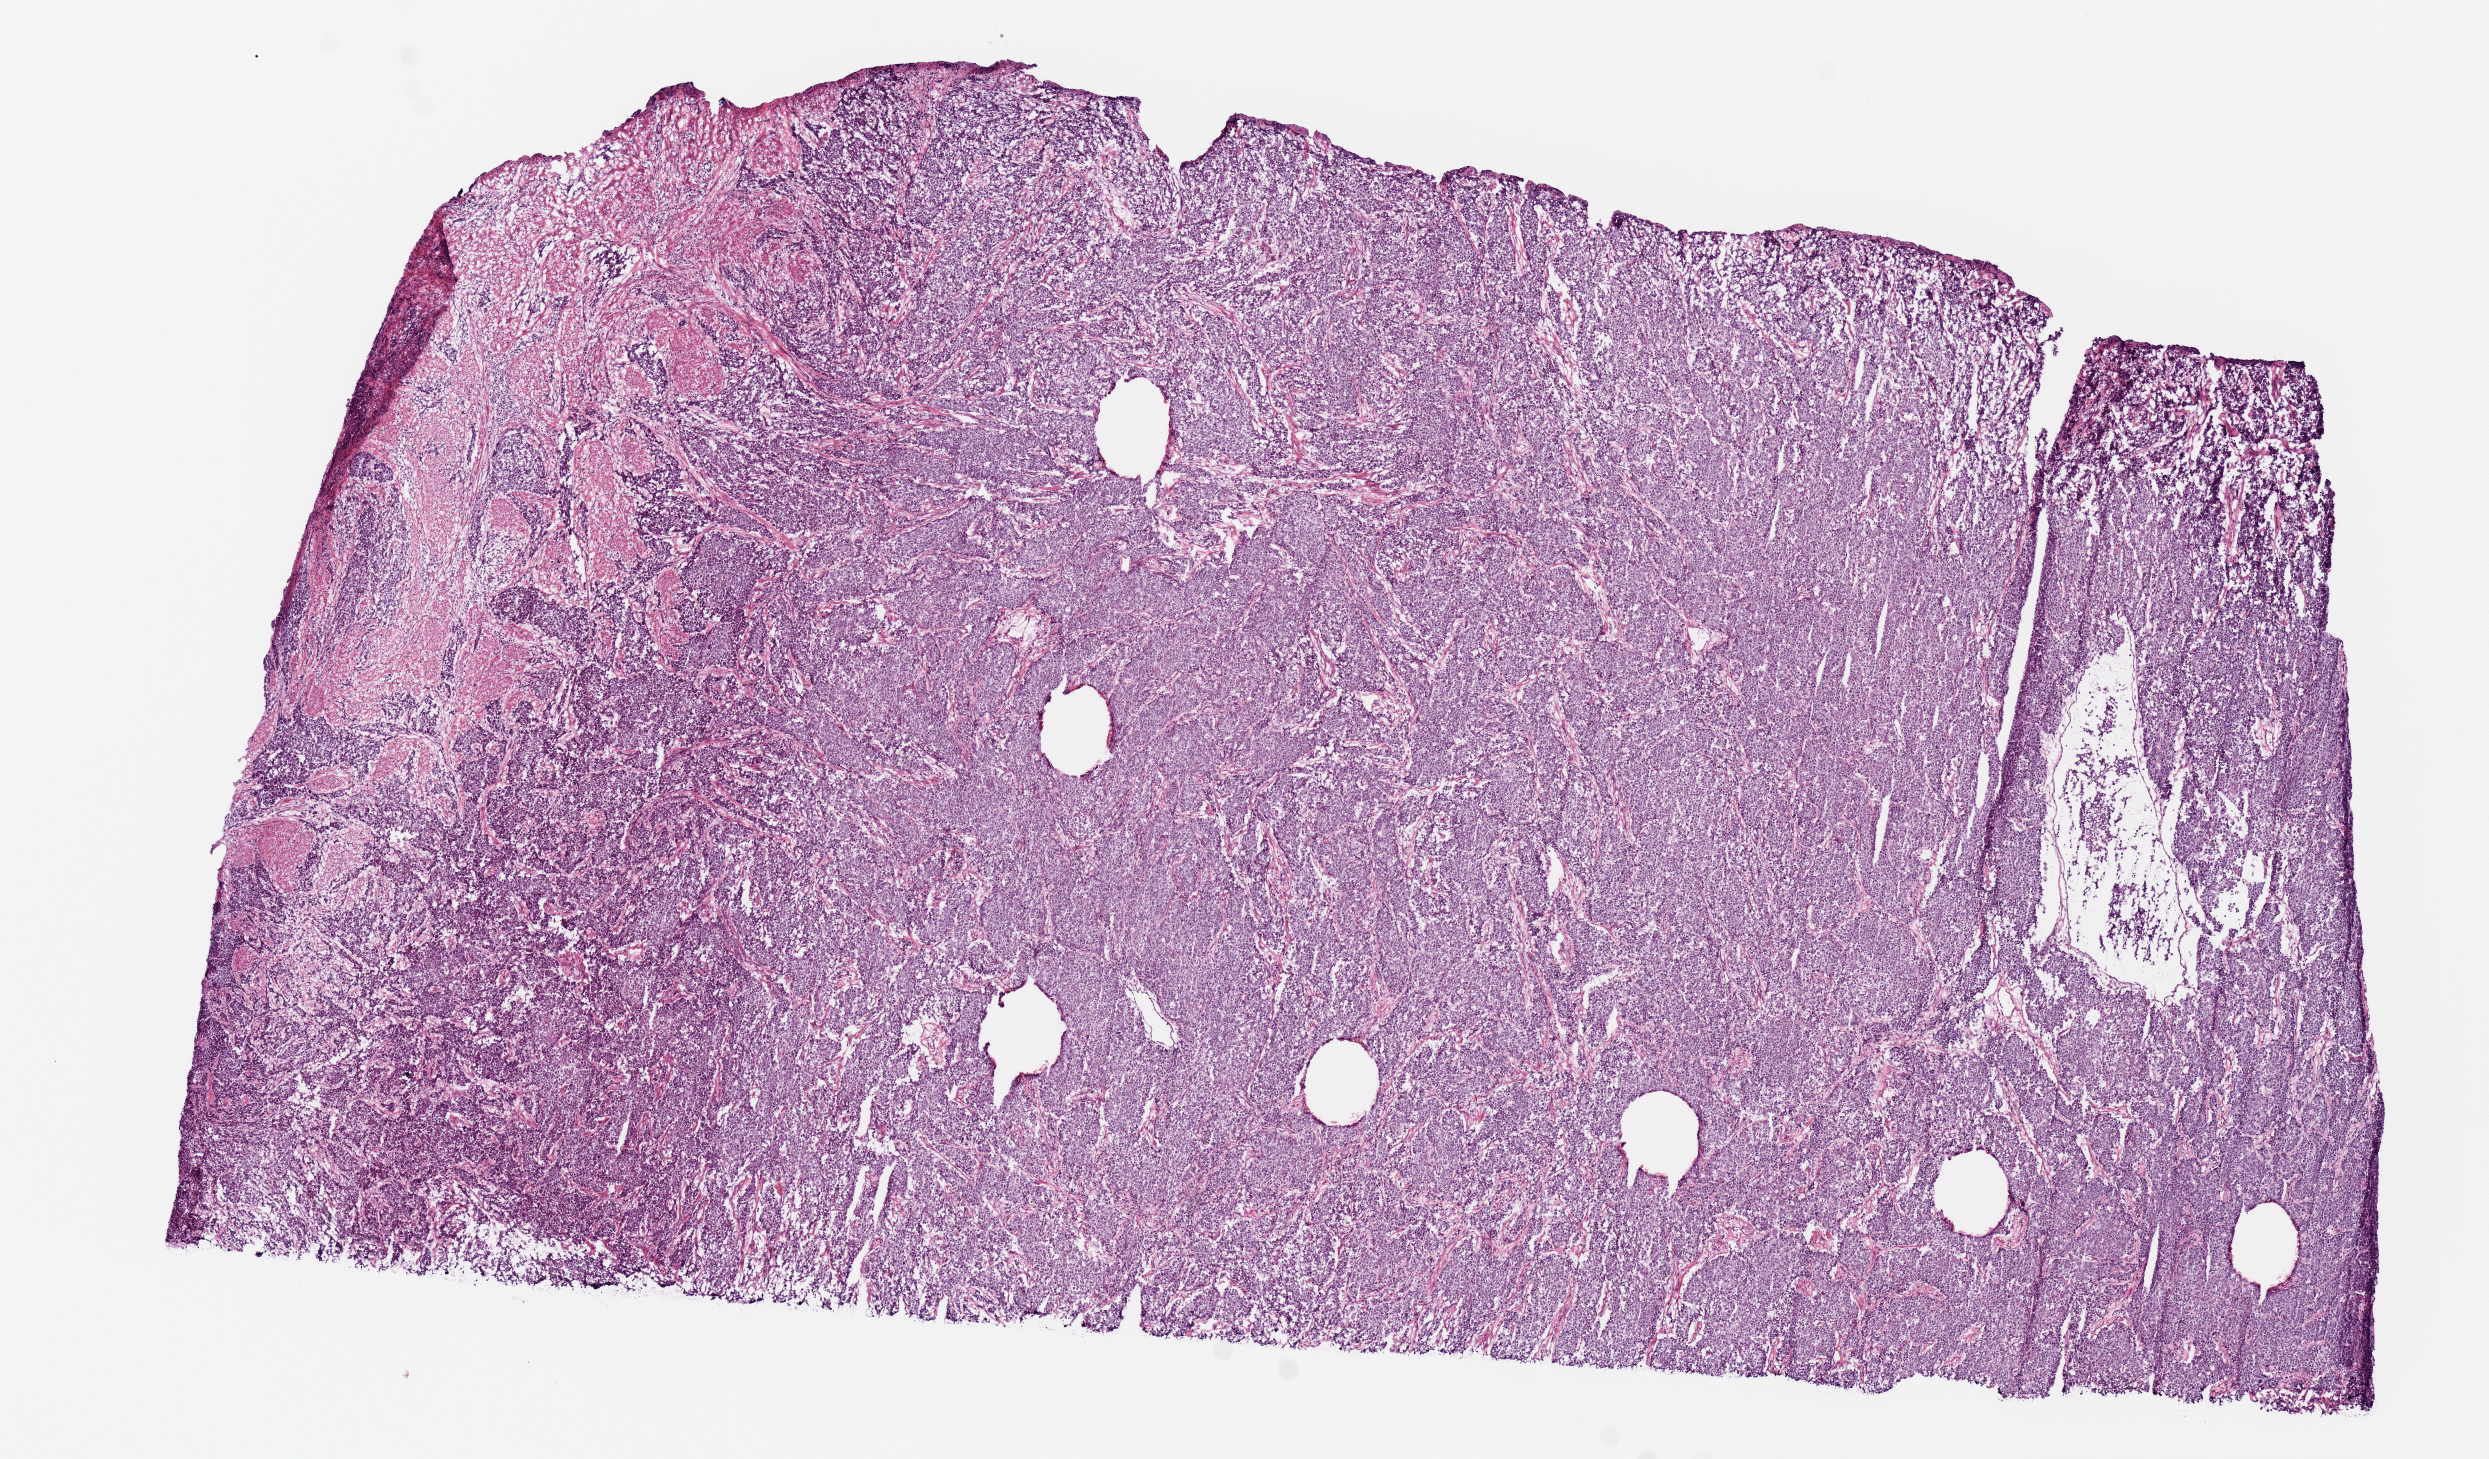
Hematoxylin and eosin (H&E) stained whole-slide image — shown as a low-resolution overview of the whole scanned area (about 9.8 x 5.8 mm), frozen section from the top of the tissue portion, uterus, primary tumour sample. Female, age 52 years at initial diagnosis. Histologic grade: G3 (poorly differentiated). Composition of this section per pathologist review: tumour cells 100%, tumour nuclei 80%, normal cells 0%, stromal cells 0%, necrosis 0%. Infiltration values recorded for this section: lymphocyte infiltration 0%, monocyte infiltration 0%, neutrophil infiltration 0%.
FIGO stage: II. Lymph nodes positive (case pathology): 0 of 7 examined. Diagnosis: Endometrioid adenocarcinoma, NOS (endometrium).